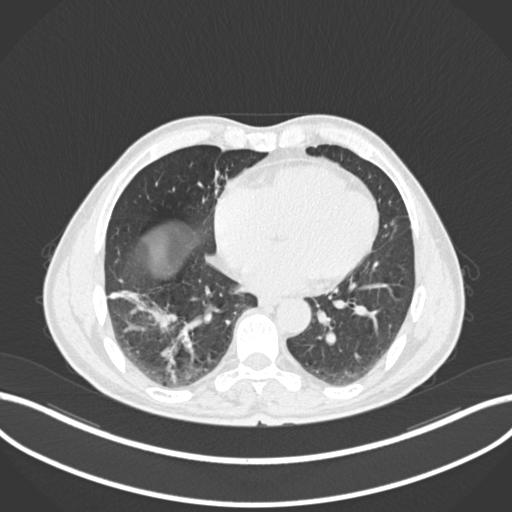
Chest CT, one axial slice; lung window (W 1500 / L -600 HU); 1 mm slice thickness; 512 × 512 image matrix, field of view 400 × 400 mm. Patient: male, 58 years. Case-level facts recorded for this patient, not image findings: clinical TNM (as recorded): T3 N0 M0; histopathological grade: G2.
Structures marked on this image (bounding box drawn by a radiologist):
- lung tumour (recorded histology: squamous cell carcinoma): bounding box <107,289,178,335> (left, top, right, bottom; pixels)